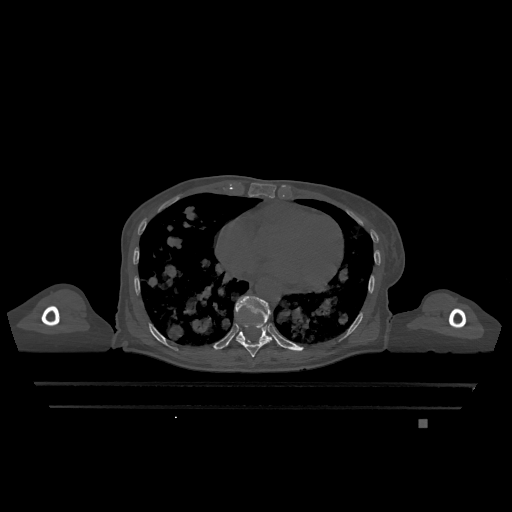
CT including the spine, one axial slice; slice 671 of 1317 in the series (ordered by position); bone window (W 1800 / L 400 HU); 0.5 mm slice thickness; 512 × 512 image matrix, field of view 500 × 500 mm. Patient: female, 74 years. From the clinical record (not read from this slice): primary cancer: lung; vertebrae with lytic lesions (as recorded): T1, T4, T5, T6, L4, L5.
Outlined on this slice (semi-automatically segmented with operator editing):
- T10 vertebra: bounding box <235,296,271,342> (left, top, right, bottom; pixels)
- T9 vertebra: <236,325,272,357>